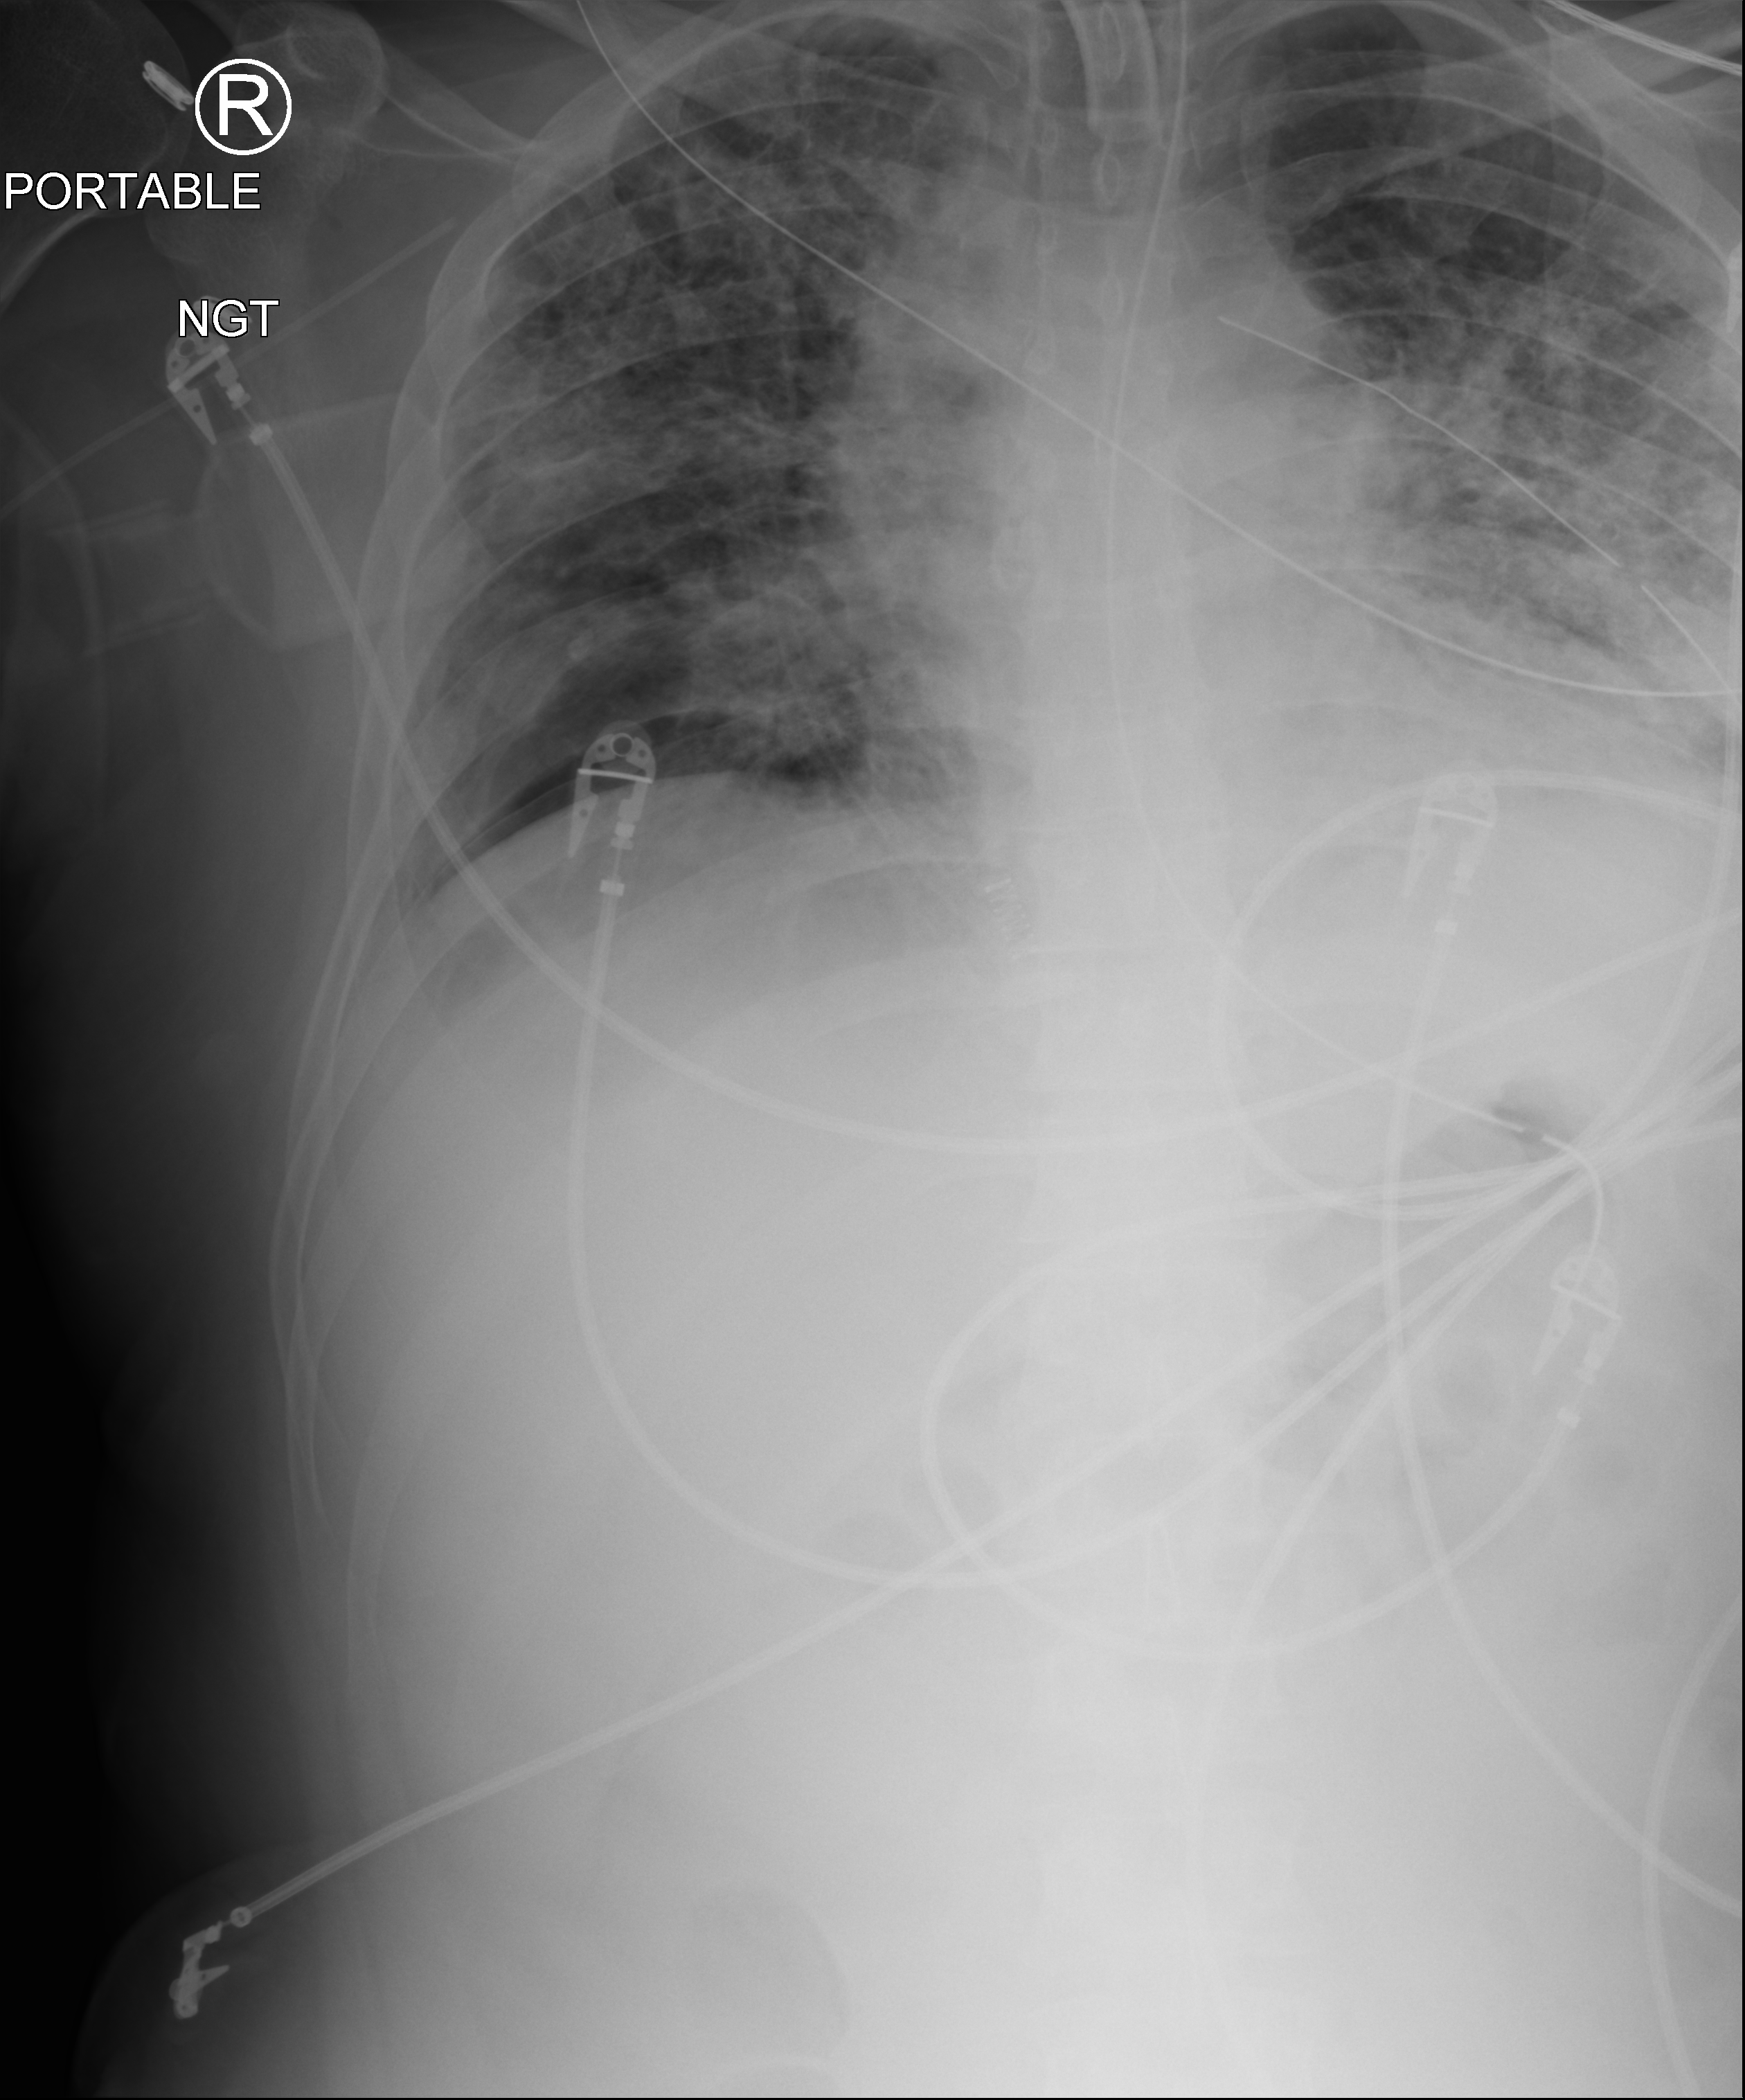
Bedside chest radiograph (computed radiography), anteroposterior (AP) projection. Patient hospitalised with COVID-19; male, aged 18–59 years.
Admission-level facts for this patient (not findings on this image; timing relative to this image not recorded): admitted to intensive care during this hospital stay: yes.